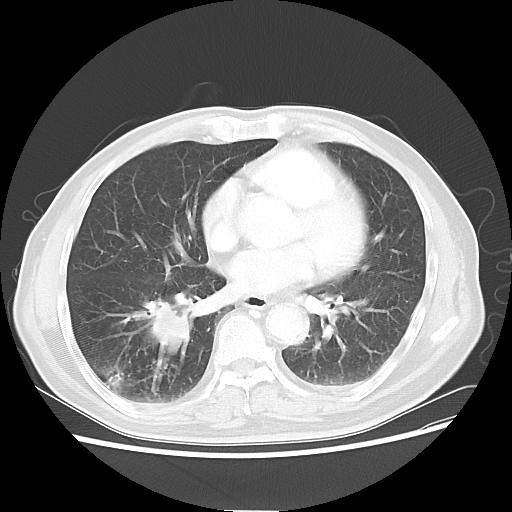
Chest CT, one axial slice; position 27 of 58 along the scan axis; reconstruction kernel LUNG; 120 kVp; lung window (W 1500 / L -600 HU); 5 mm slice thickness; 512 × 512 image matrix, field of view 360 × 360 mm. Male patient, age 74 years. From the clinical record (not read from this slice): clinical TNM (as recorded): T1c N1 M1.
Outlined on this slice (bounding box drawn by a radiologist):
- lung tumour (recorded histology: adenocarcinoma): bounding box <121,293,194,363> (left, top, right, bottom; pixels)